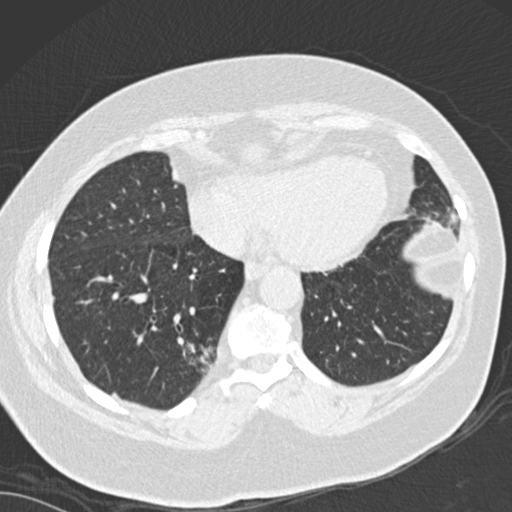
Low-dose screening chest CT, one axial slice; lung window (W 1500 / L -600 HU); 2 mm slice thickness; 512 × 512 image matrix, field of view 328 × 328 mm.
Outlined on this slice (expert manual segmentation):
- lesion 1 (tumor, lower lobe of right lung): box from (x=183, y=341) to (x=212, y=372) px